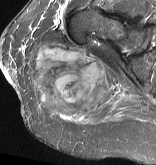
MRI of an extremity soft-tissue mass, one axial slice; position 34 of 57 along the scan axis; STIR; MR volume resampled by the dataset authors to the PET/CT grid (not the native acquisition matrix); 3.27 mm slice thickness; 156 × 165 image matrix. Female patient. Case-level facts recorded for this patient, not image findings: histological type: epithelioid sarcoma with vascular differentiation; site of the primary tumour: right buttock.
Structures marked on this image (expert contour drawn on MRI and transferred to this co-registered scan by the dataset authors):
- gross tumour volume (mass): box from (x=29, y=42) to (x=112, y=120) px